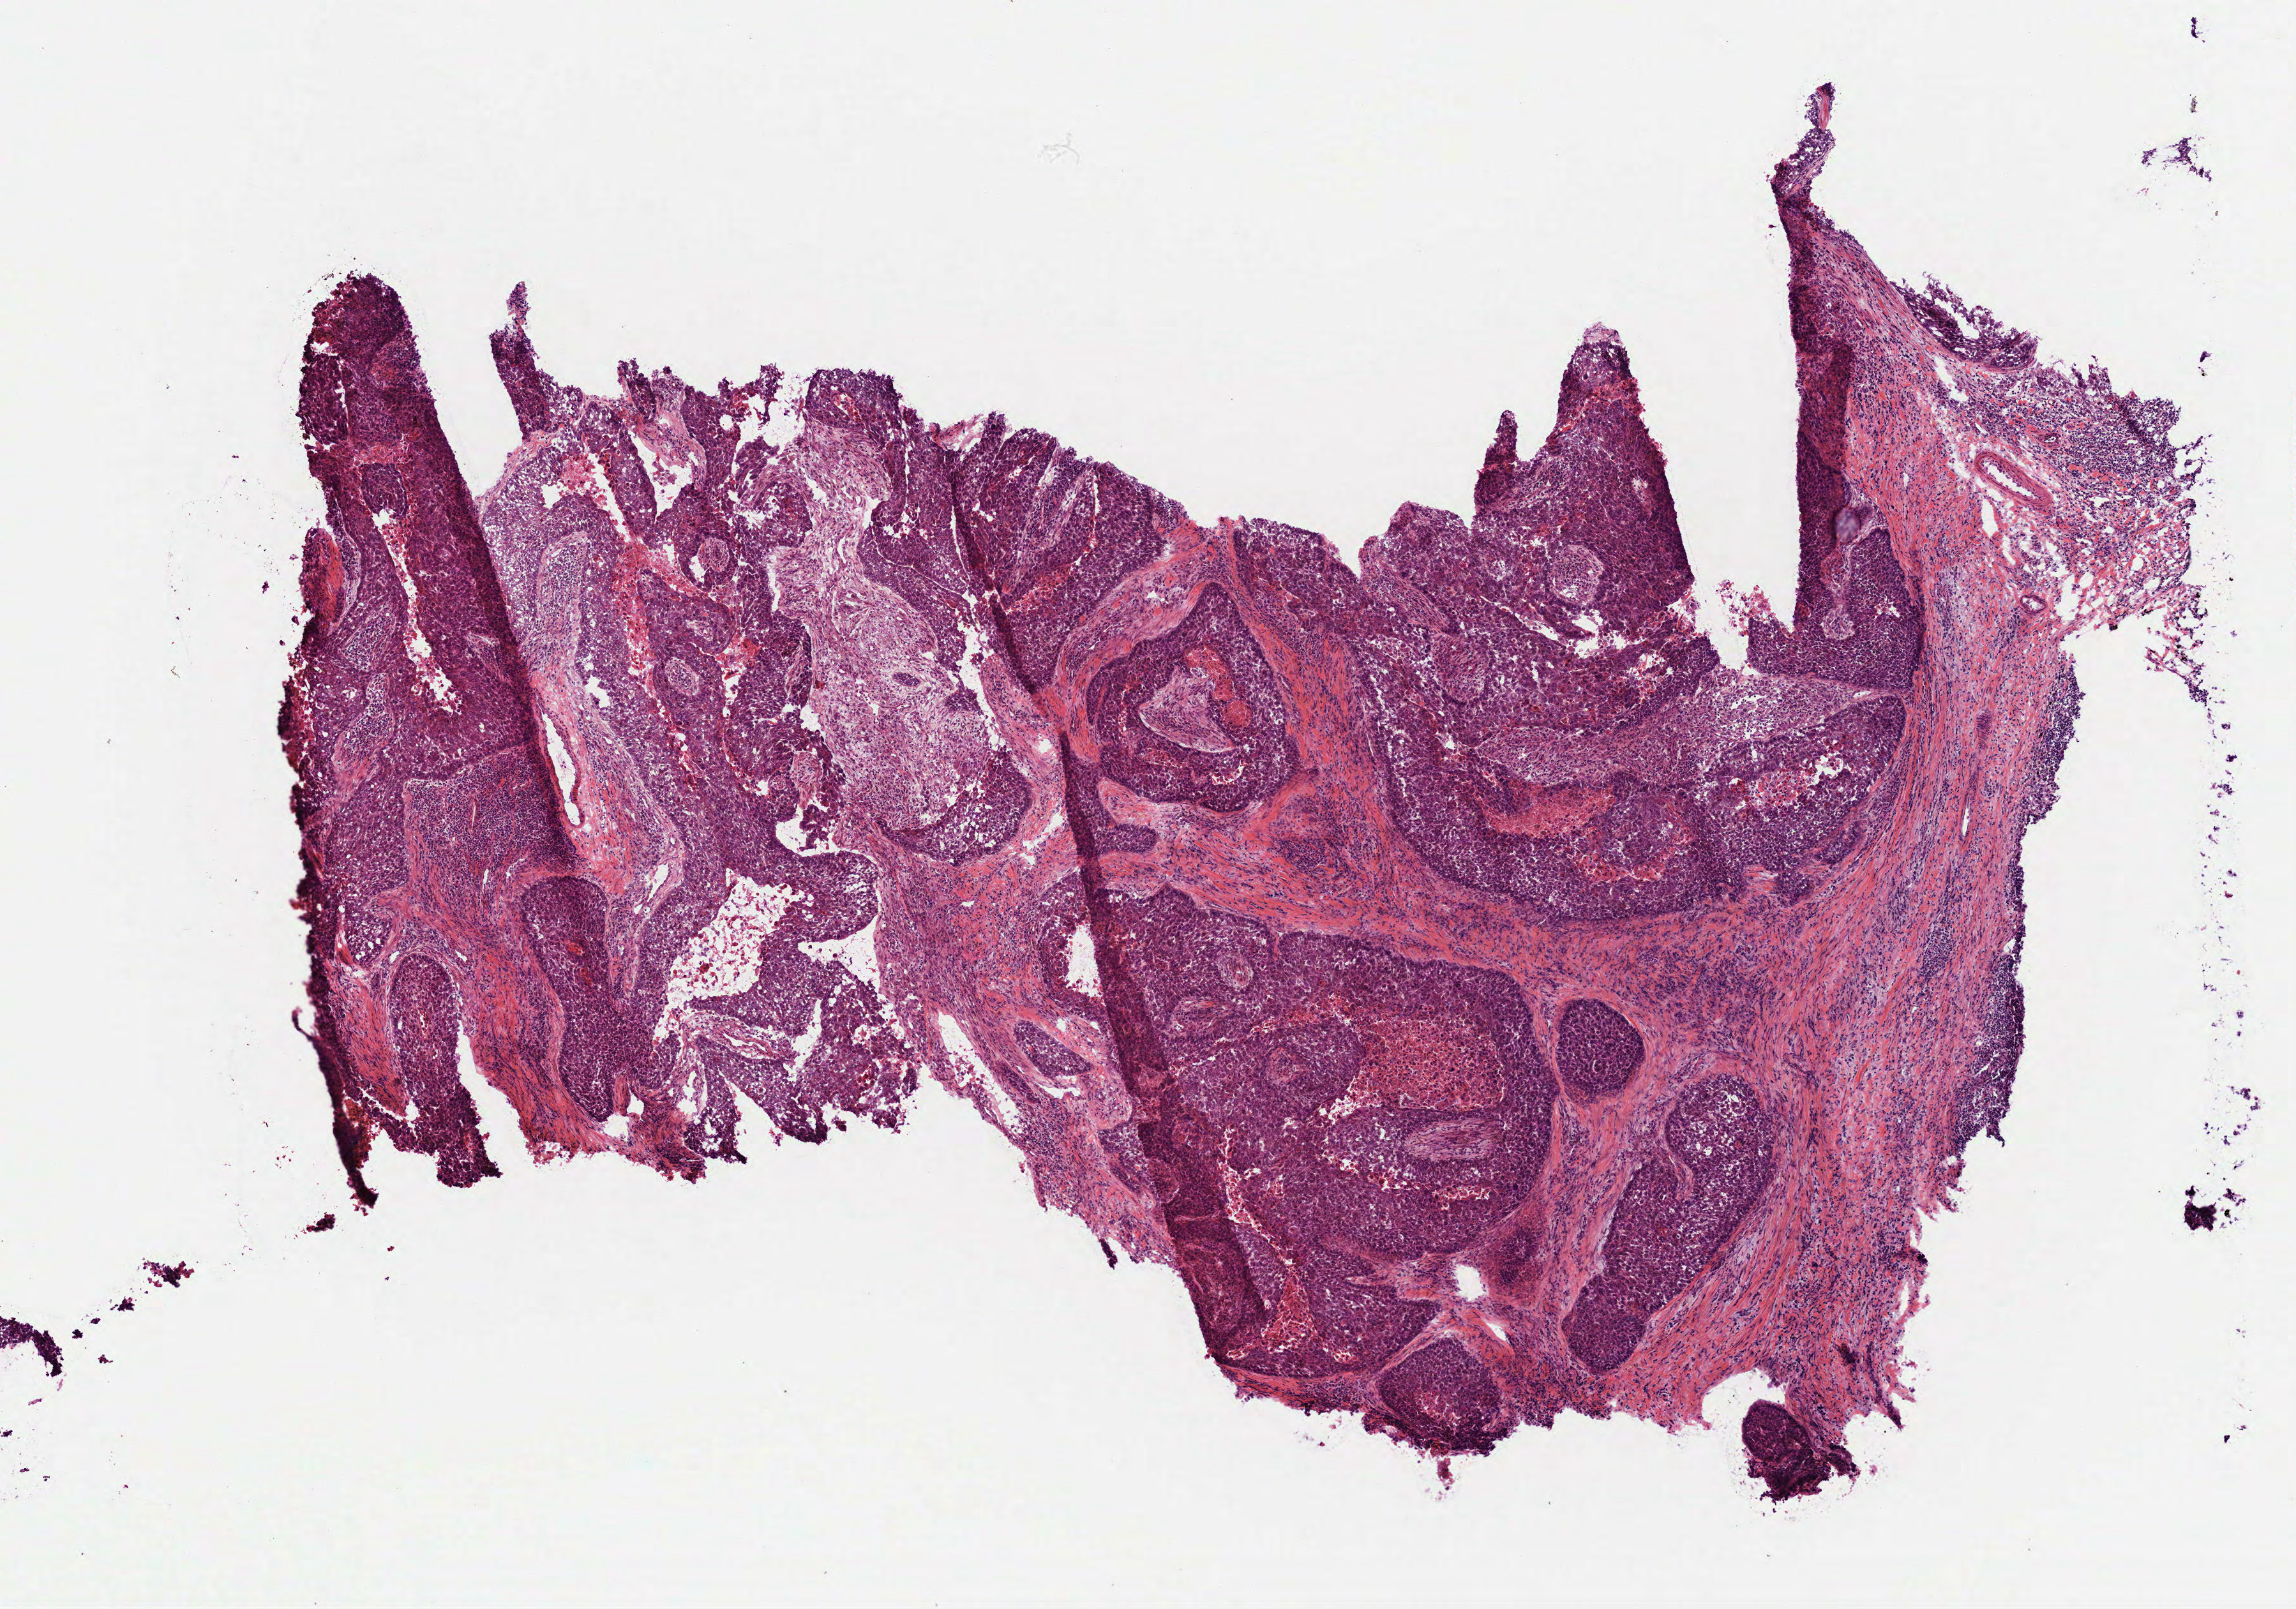
Digitized H&E-stained tissue section (whole slide) — low-resolution overview of the scanned area, about 7.3 x 5.1 mm (slide scanned at 40x). Frozen section from the bottom of the tissue portion. Sample: primary tumour, lung. Male patient; age at initial diagnosis 56 years. Slide review estimates, as recorded: tumour cells 70%, tumour nuclei 65%, normal cells 0%, stromal cells 30%, necrosis 0%.
AJCC pathologic stage: IIB (6th edition). Diagnosis: Squamous cell carcinoma, NOS (lower lobe, lung). Laterality: right.